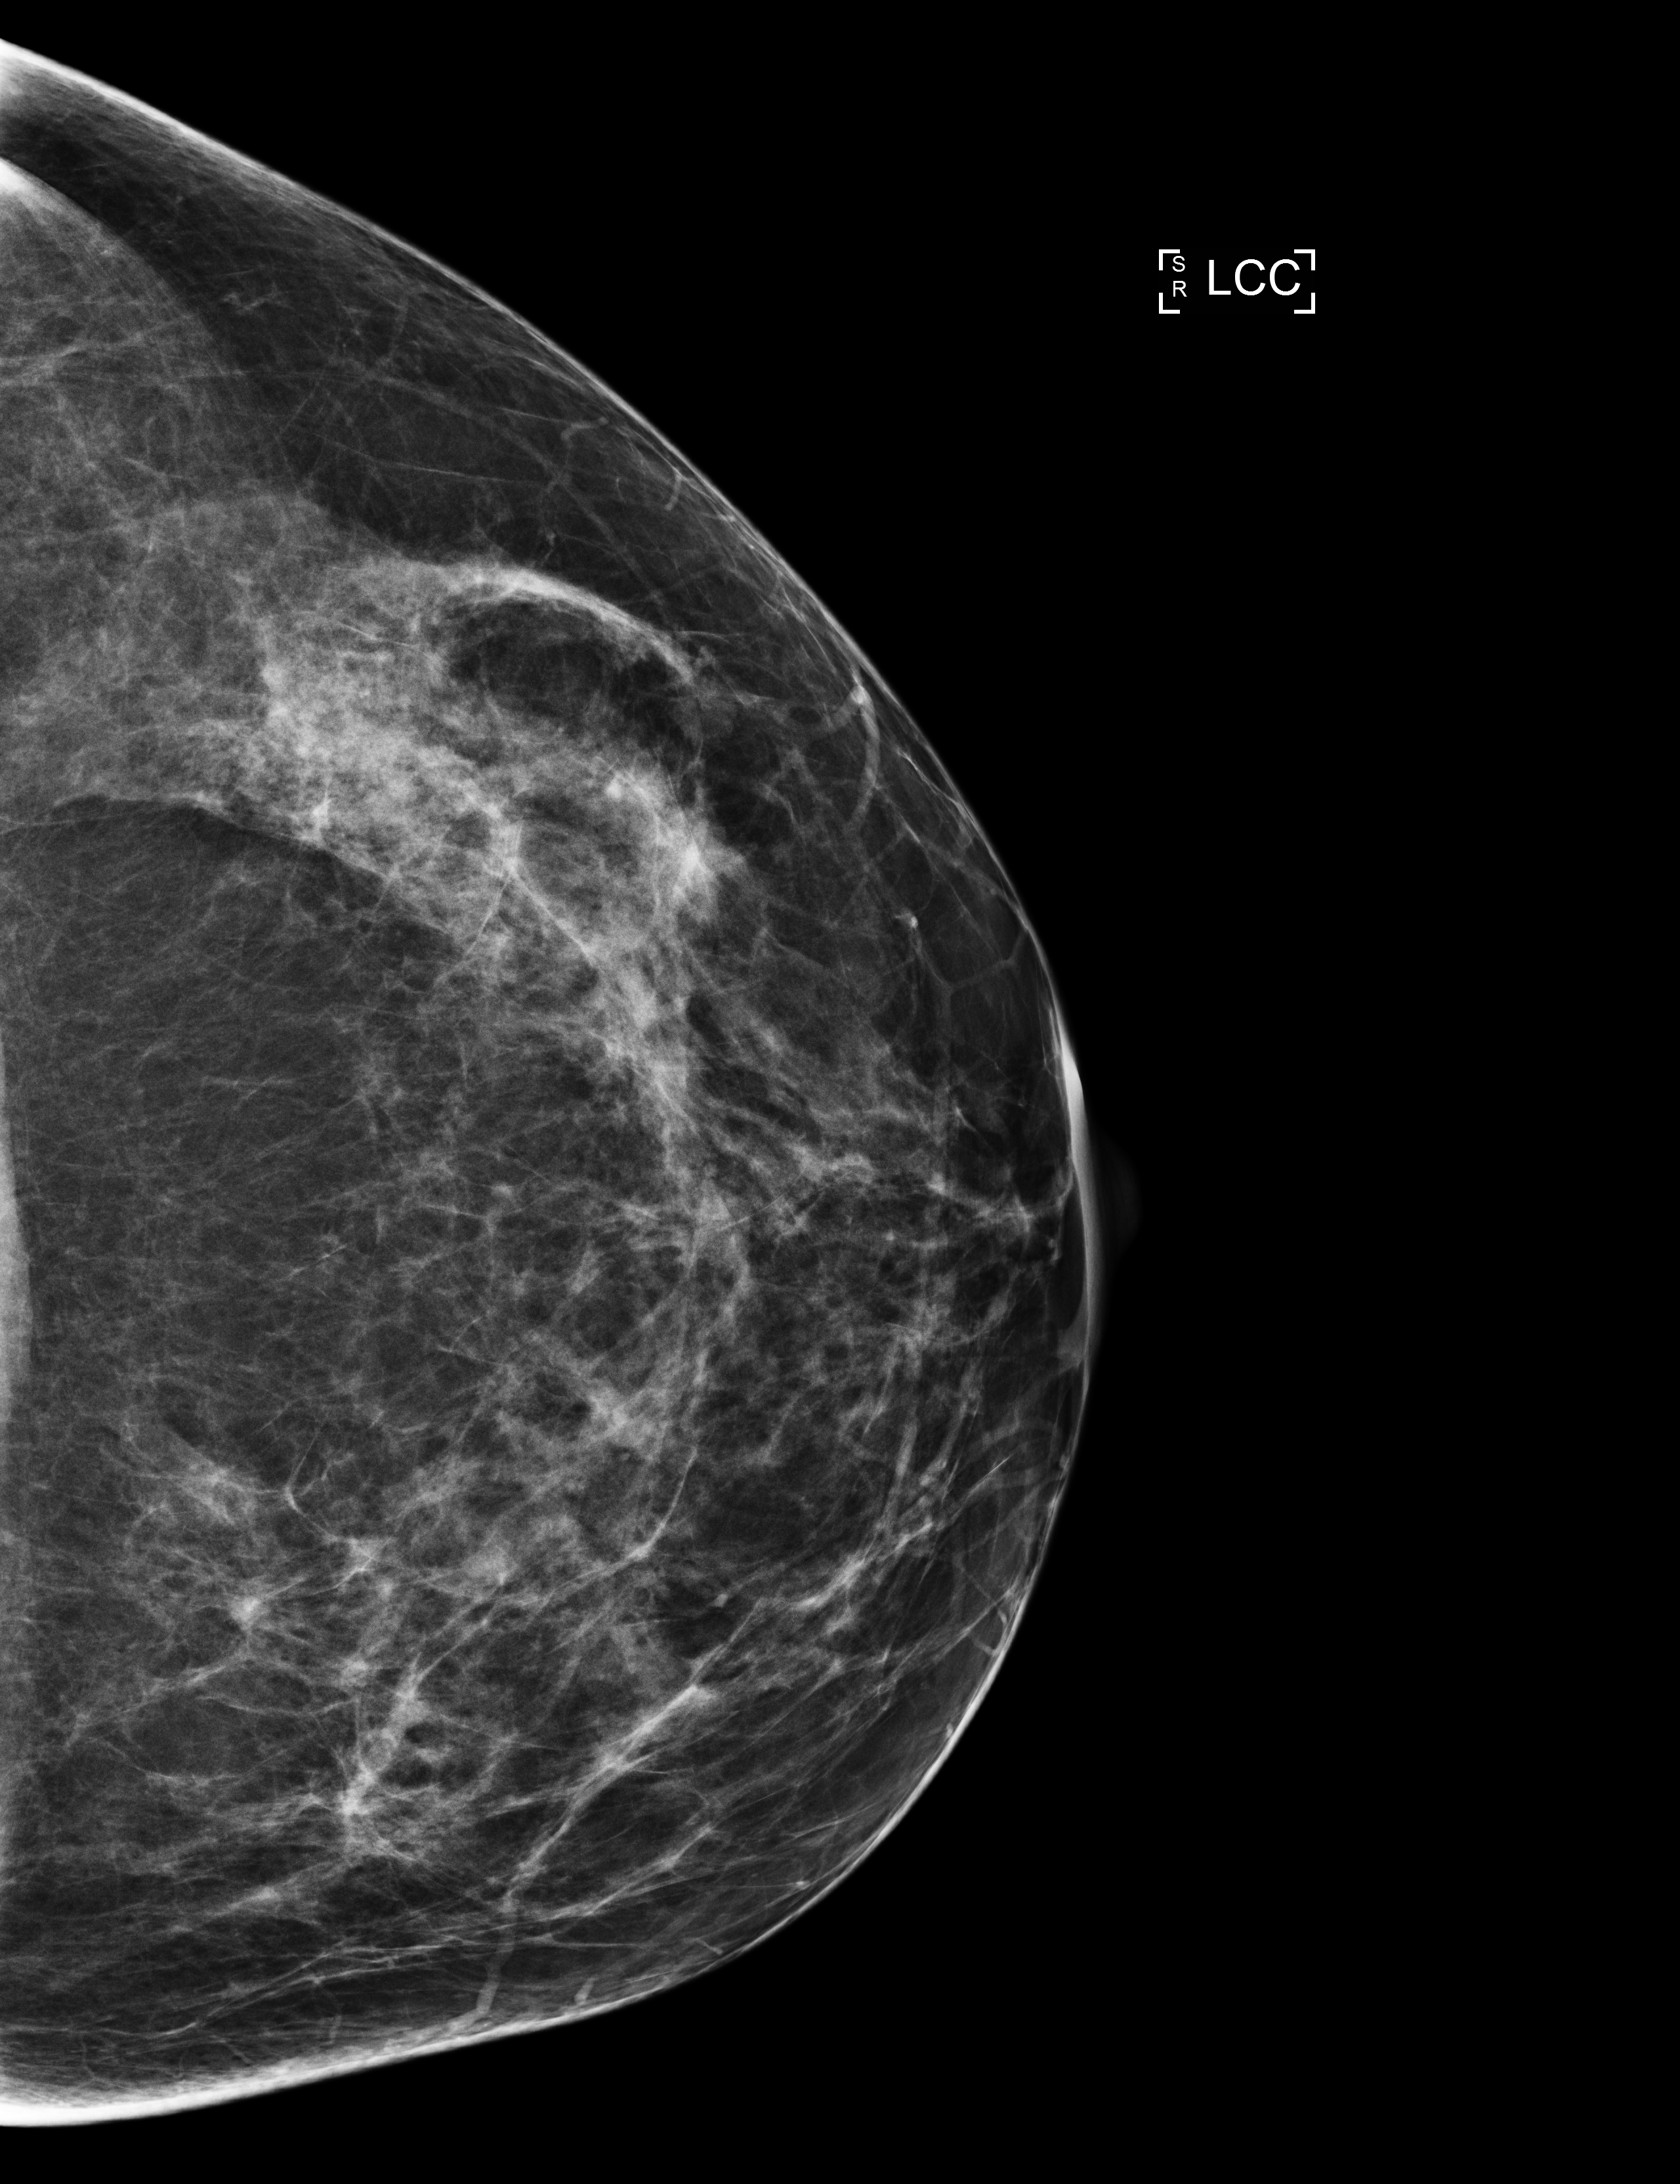
Digital mammogram (FFDM), left breast, cranio-caudal projection, annual screening mammography examination, compressed breast thickness 70 mm, system: Selenia Dimensions. Female patient, age 50 years.
- breast density at the screening exam (both breasts): heterogeneously dense (BI-RADS density category c)
- final BI-RADS assessment for this screening round (tomosynthesis exam, both breasts): category 1
- recall: no recall after this screen